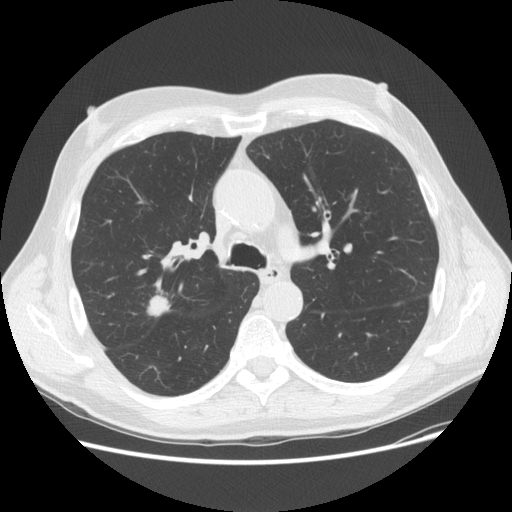
Low-dose screening chest CT, one axial slice. 120 kVp. Lung window (W 1500 / L -600 HU). 2.5 mm slice thickness. 512 × 512 image matrix, field of view 380 × 380 mm.
Annotated regions visible in this slice (expert manual segmentation):
- lesion 1 (tumor, upper lobe of right lung): bounding box <147,294,171,317> (left, top, right, bottom; pixels)